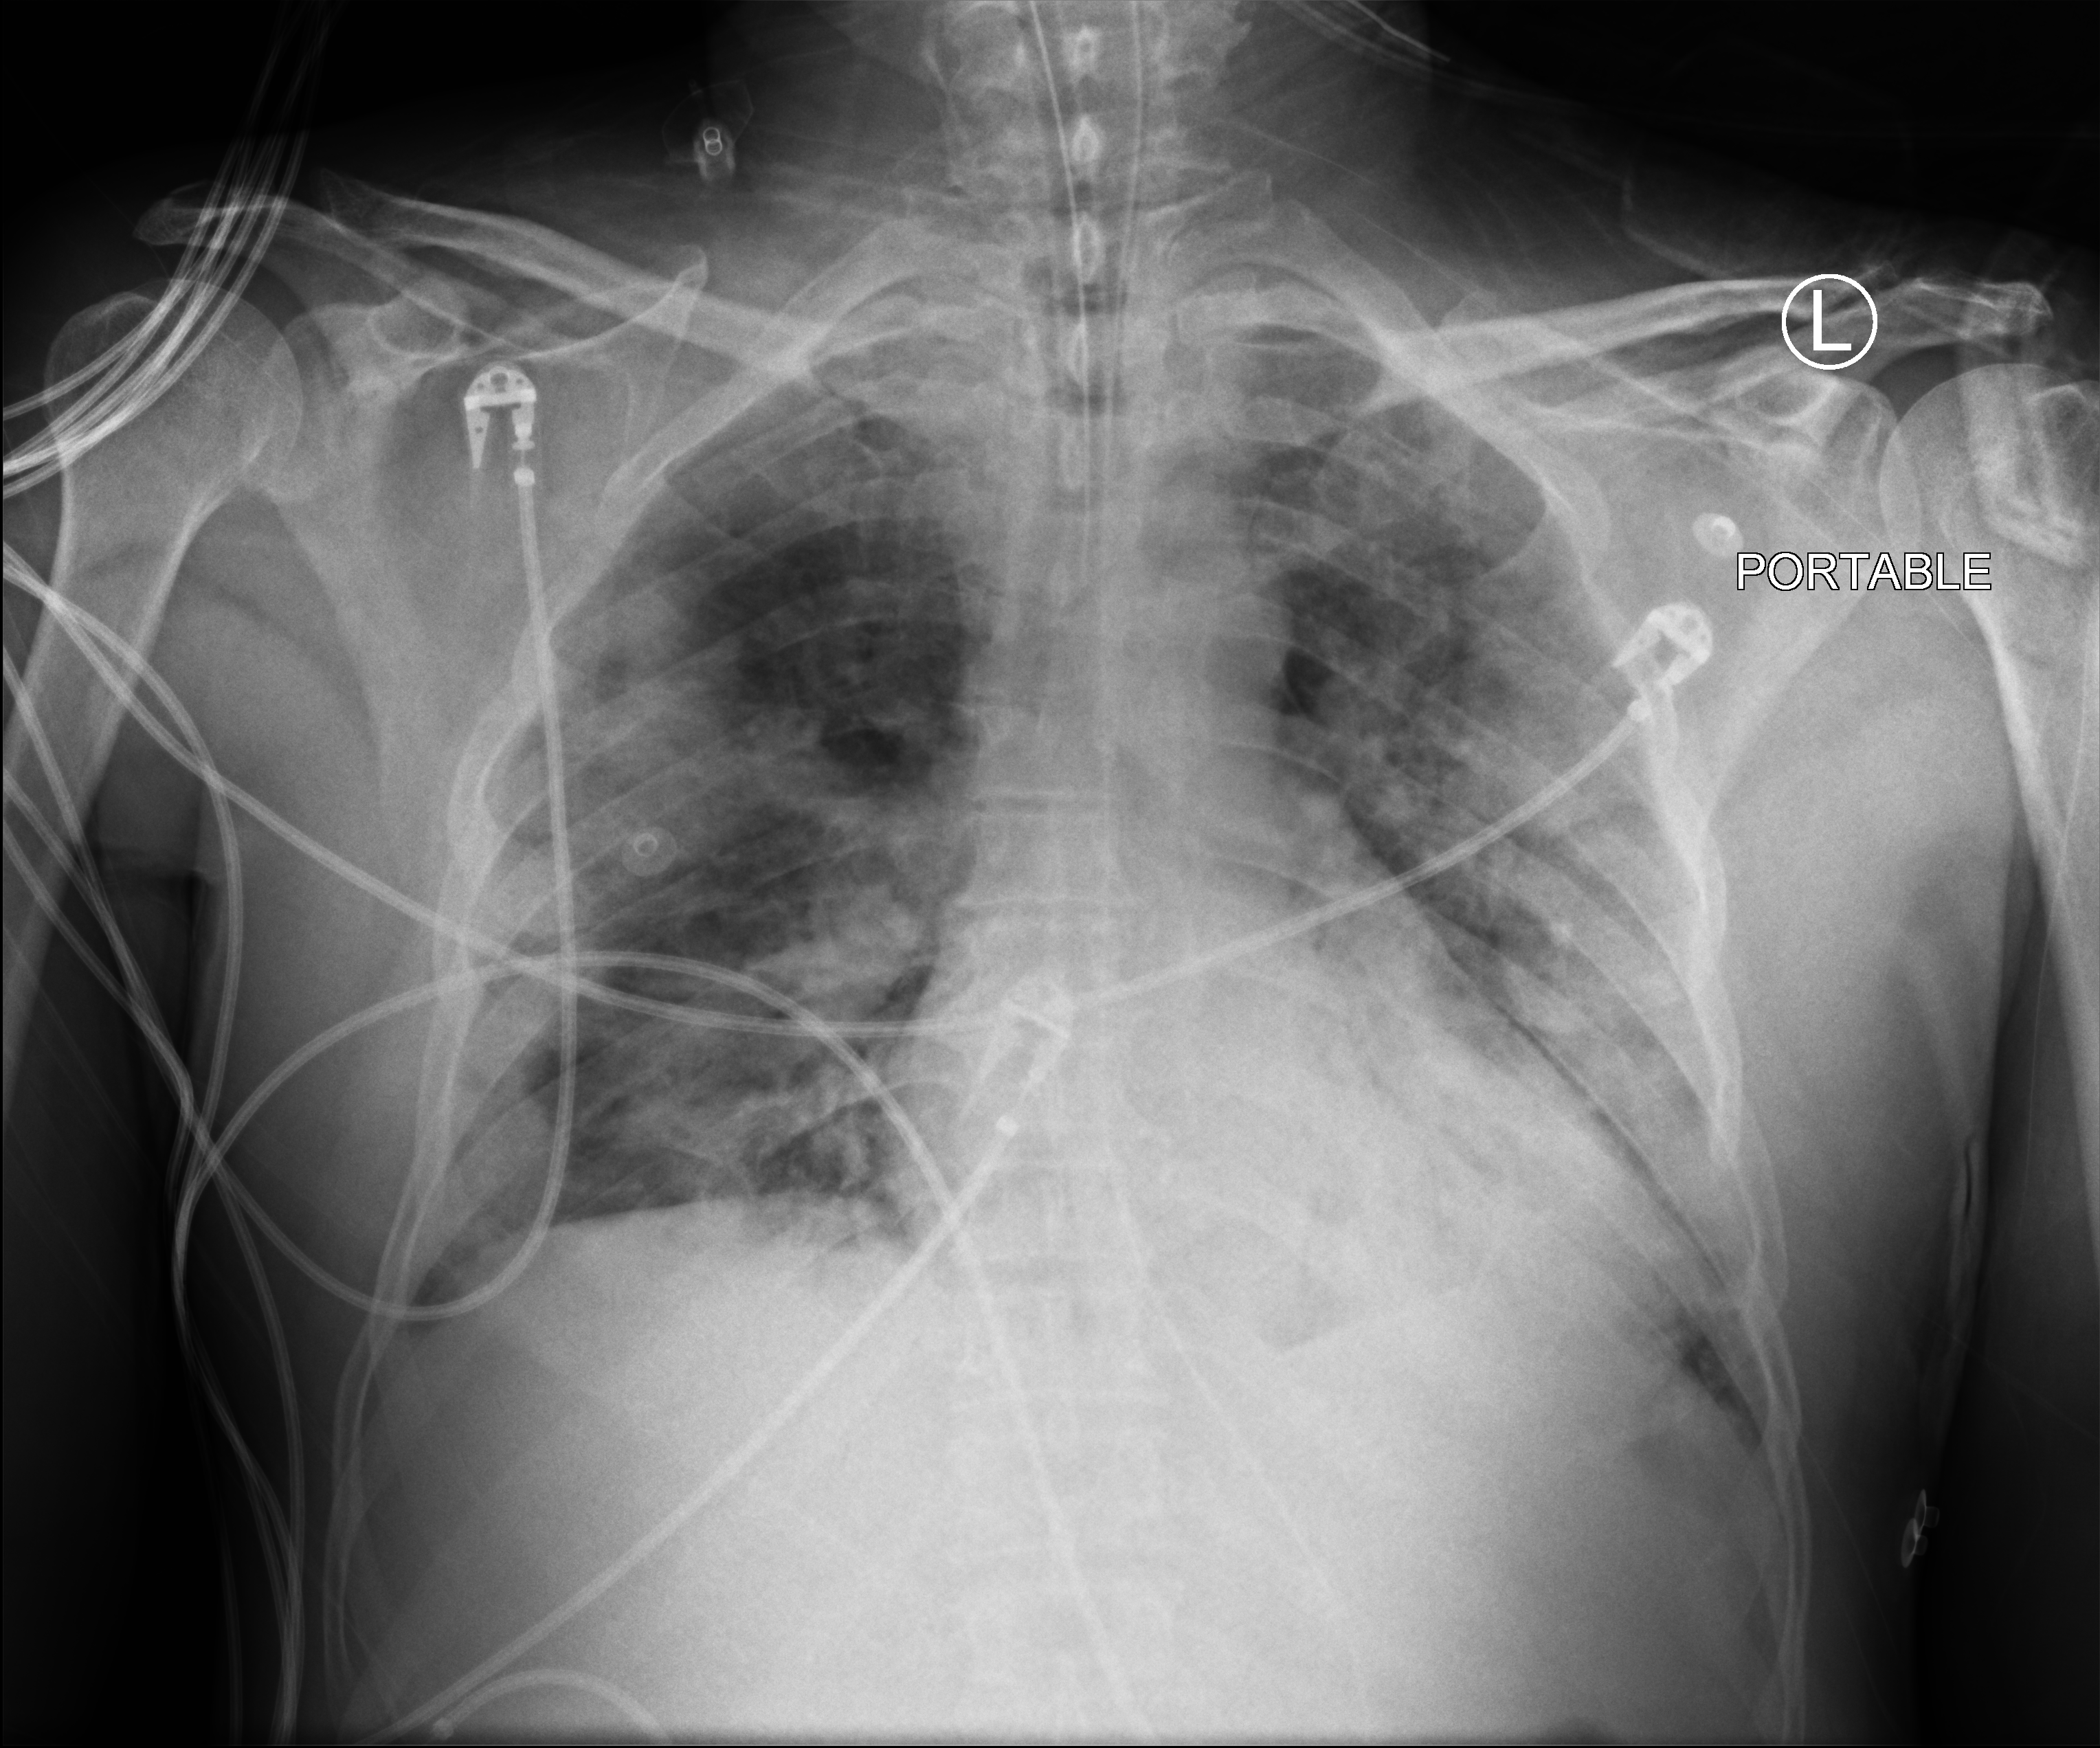
Chest X-ray (portable), anteroposterior (AP) projection. Patient hospitalised with COVID-19; male, aged 18–59 years.
Admission-level facts for this patient (not findings on this image; timing relative to this image not recorded): diabetes (admission record): no.